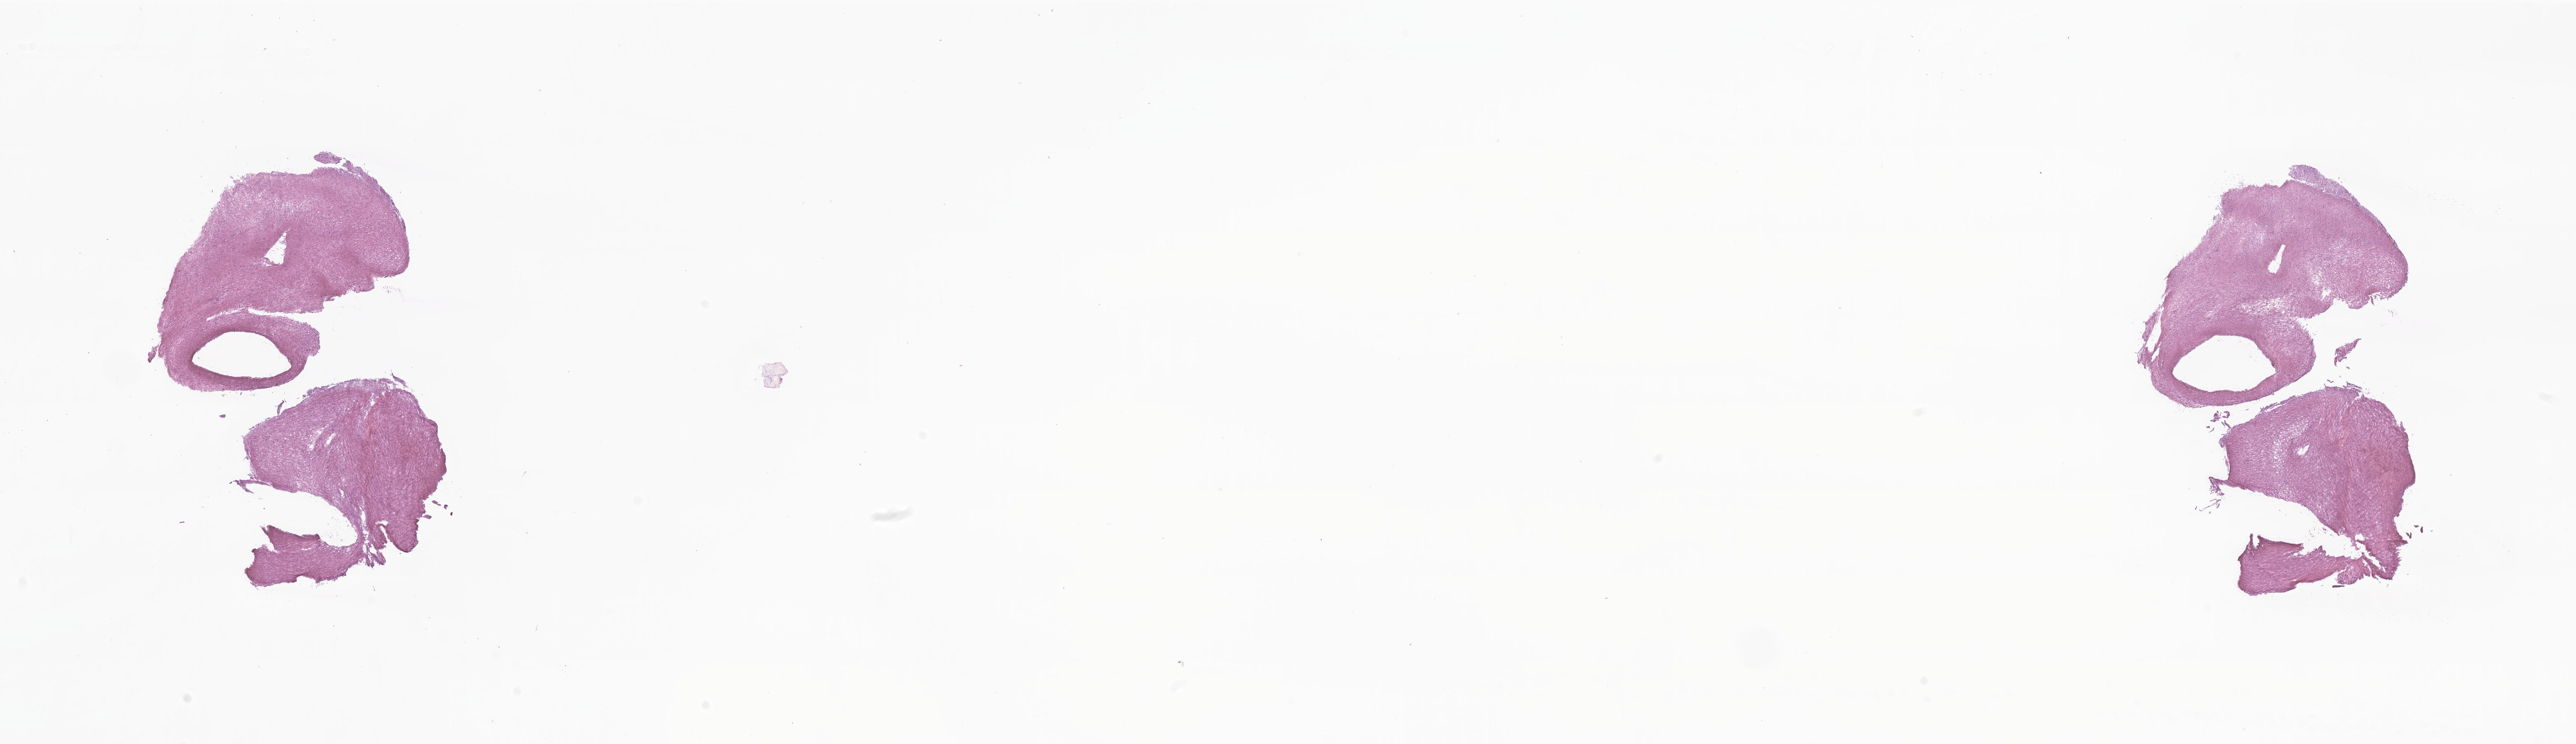
H&E whole-slide image of tumor tissue from the brain — shown as a low-resolution overview of the whole scanned area (about 32.1 x 9.3 mm), cryosection (OCT / tissue freezing medium). Patient male; age 206 months (17 years 2 months).
Diagnosis: Astrocytoma, NOS.